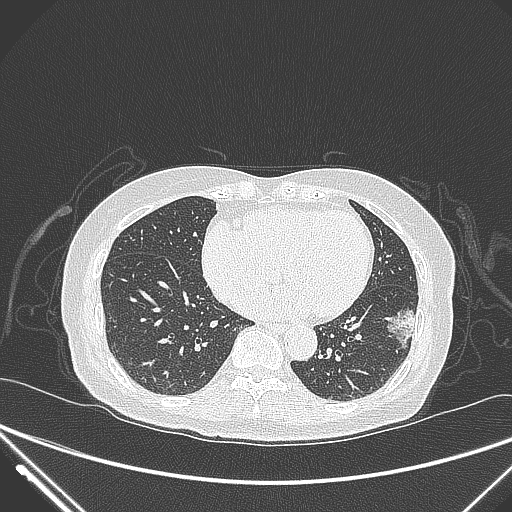
Chest CT, one axial slice. Slice 112 of 310 in the series (ordered by position). Lung window (W 1500 / L -600 HU). 1 mm slice thickness. 512 × 512 image matrix, field of view 377 × 377 mm. Female patient, age 82 years. From the clinical record (not read from this slice): clinical TNM (as recorded): T1c N0 M0; histopathological grade: G2.
Annotated regions visible in this slice (bounding box drawn by a radiologist):
- lung tumour (recorded histology: adenocarcinoma): bounding box <385,303,425,356> (left, top, right, bottom; pixels)